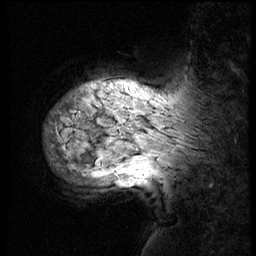
Breast MRI (dynamic contrast-enhanced), one sagittal slice. Position 45 of 56 along the scan axis. 3 images stored at this slice position (order not interpretable as contrast timing). 1.5 T. TE 4.2 ms, TR 8.9 ms. 3 mm slice thickness. 256 × 256 image matrix, field of view 220 × 220 mm. Patient: female, 57 years. Case-level facts recorded for this patient, not image findings: setting: breast cancer imaged before/during neoadjuvant chemotherapy; receptor status: HER2-positive.
Structures marked on this image (semi-automatic segmentation, software-assisted and operator-edited):
- analysis volume of interest (the breast-tissue region the enhancement analysis was run in; not a lesion): bounding box [x1, y1, x2, y2] px = [45, 70, 223, 156]
- tumour enhancement mask (voxels above the 140 % enhancement threshold inside the analysis volume of interest): [112, 83, 113, 87]